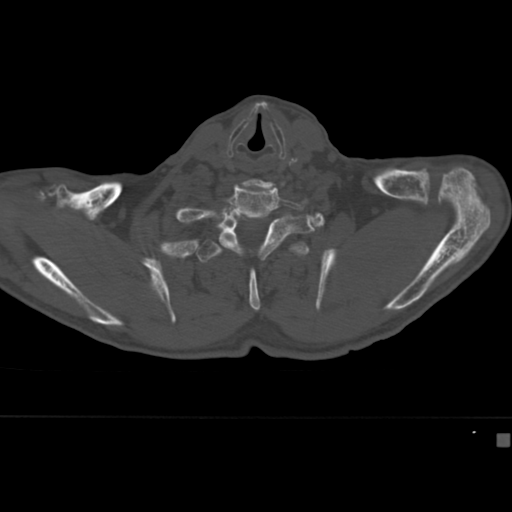
CT including the spine, one axial slice; slice 351 of 430 in the series (ordered by position); reconstruction kernel Br40s; bone window (W 1800 / L 400 HU); 1.5 mm slice thickness; 512 × 512 image matrix. Patient: male, 64 years. From the clinical record (not read from this slice): primary cancer: uterus.
Structures marked on this image (semi-automatically segmented with operator editing):
- T2 vertebra: bounding box (x1, y1, x2, y2) in pixels: (196, 240, 310, 311)